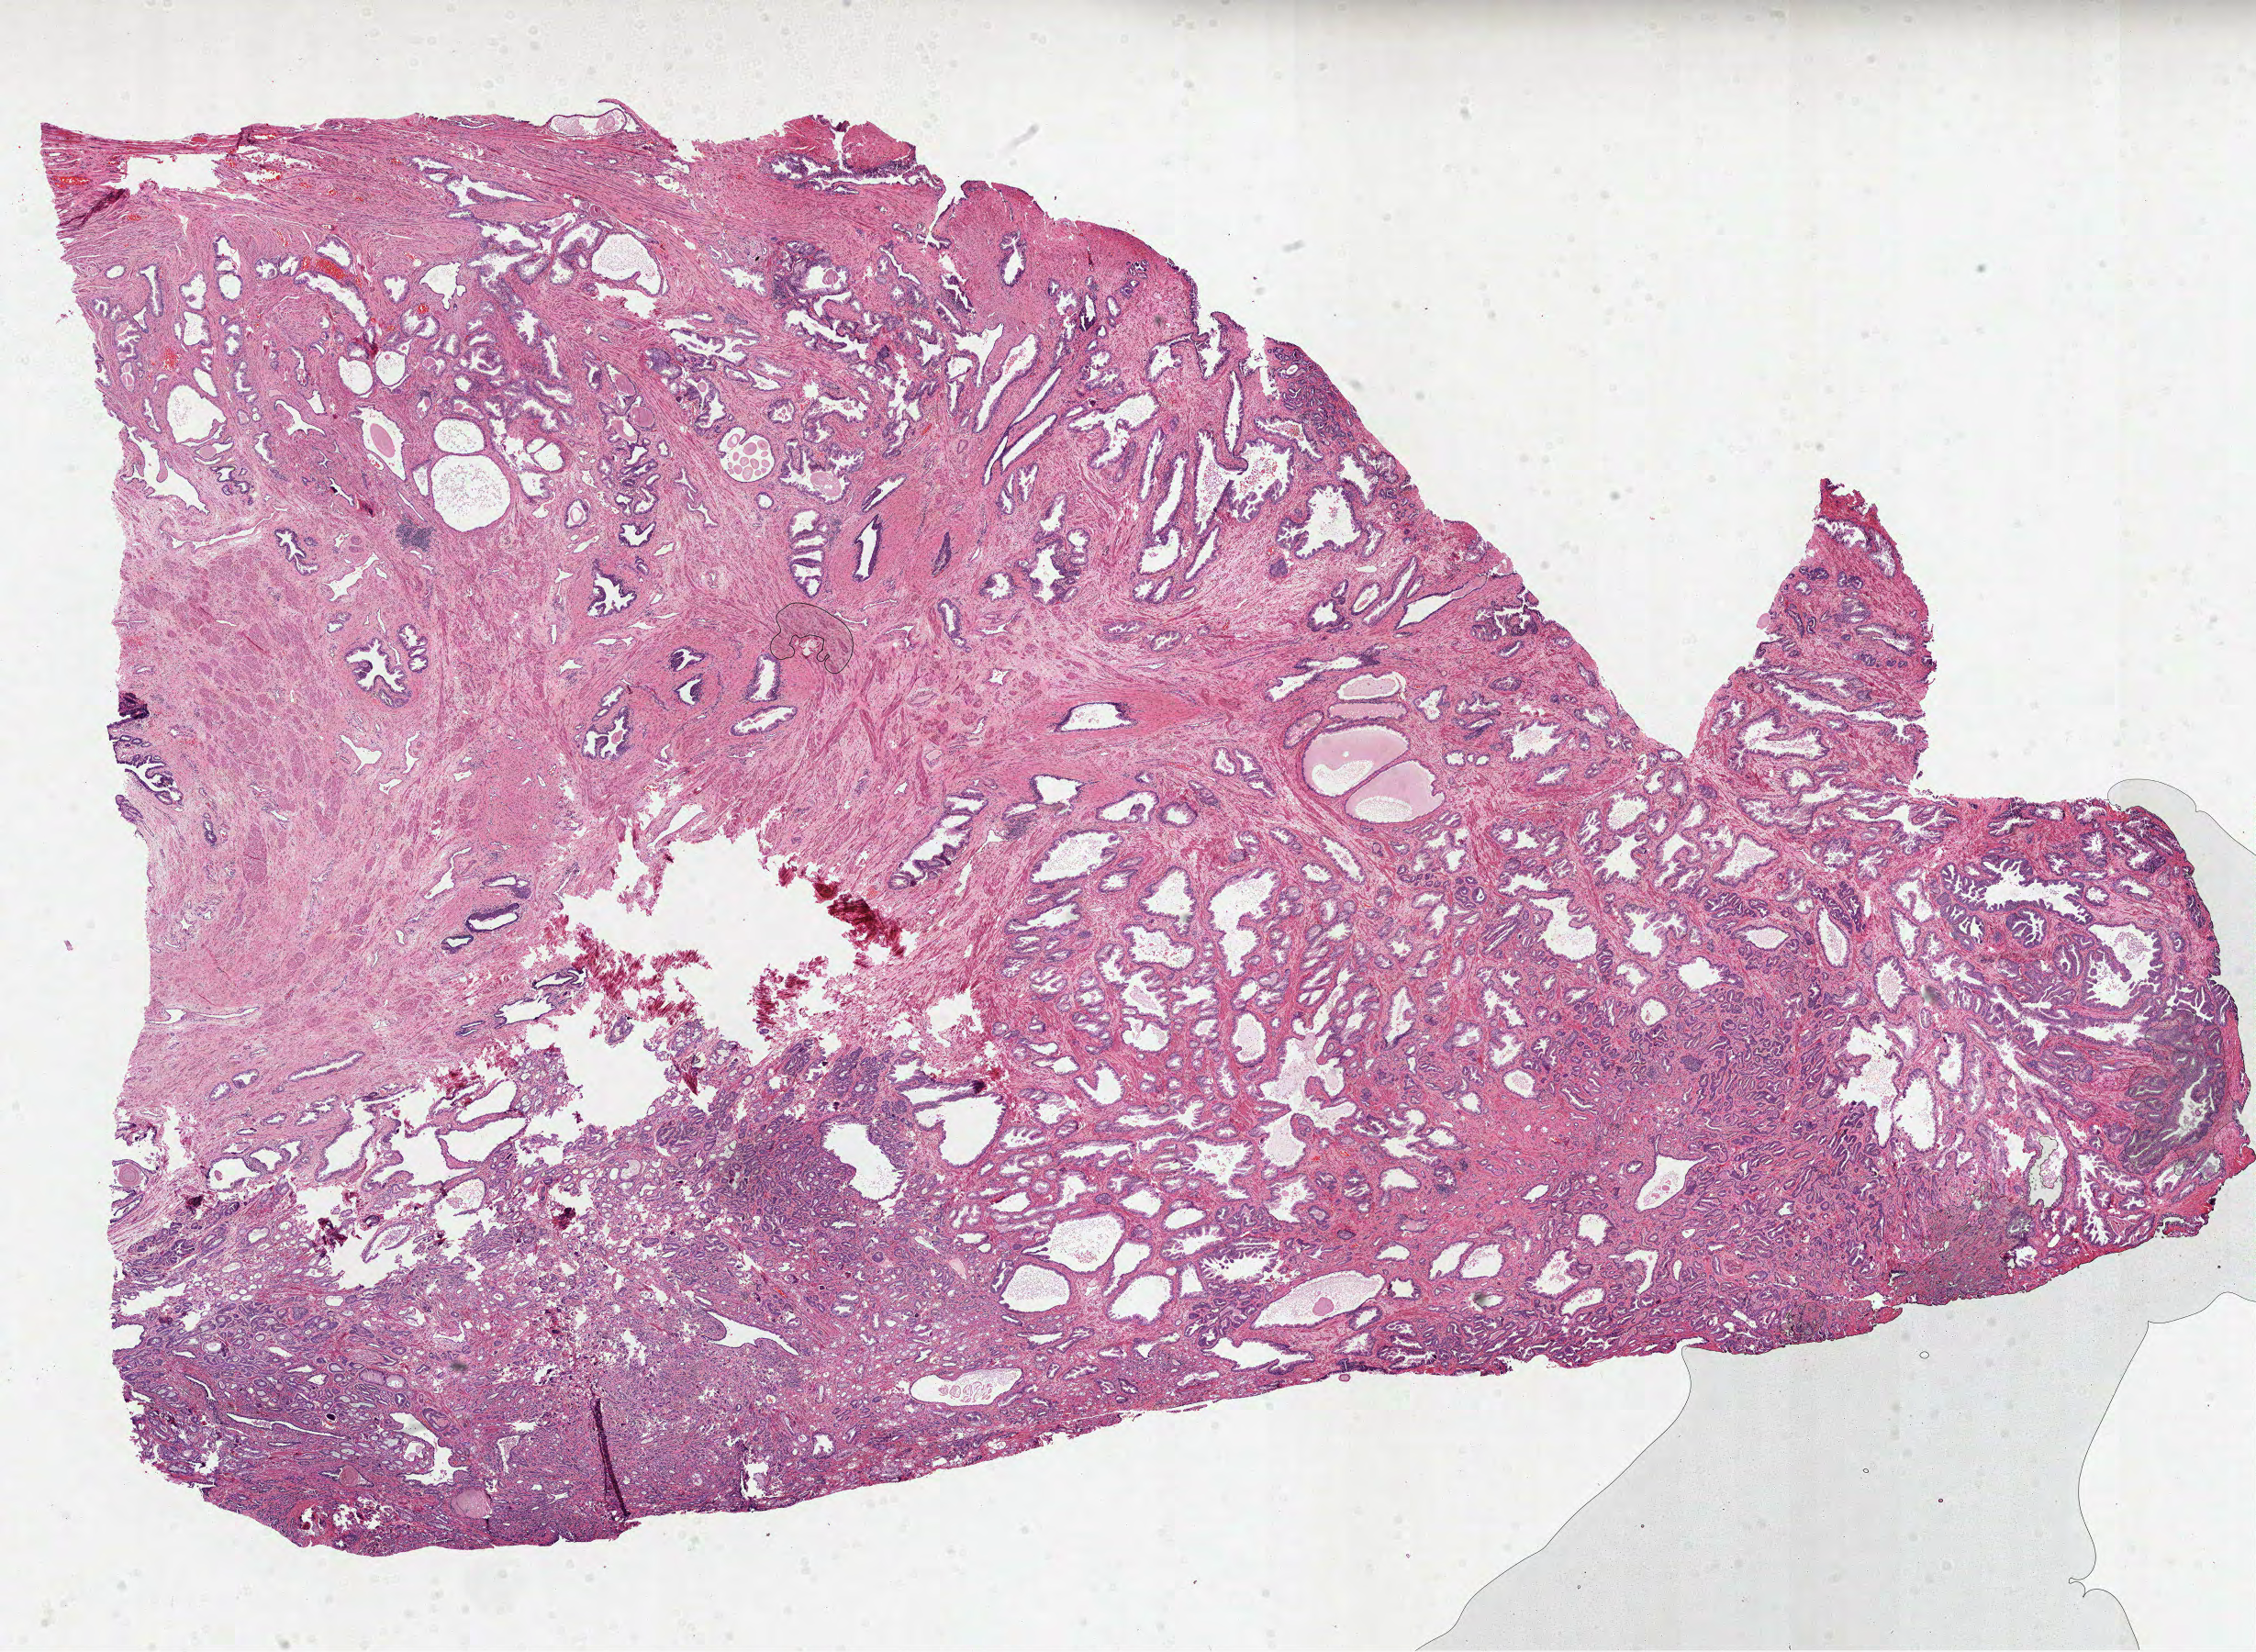
Whole-slide histology image, Hematoxylin and eosin (H&E) stained, shown as a low-resolution overview of the whole scanned area (about 19.8 x 14.5 mm), formalin-fixed paraffin-embedded (FFPE) diagnostic section, prostate, primary tumour sample. Patient: male, age at initial diagnosis 59 years. Gleason score: 7 (3+4).
* lymph nodes positive (case pathology): 0 of 26 examined
* pathologic diagnosis: Acinar cell carcinoma (prostate gland)
* laterality: bilateral